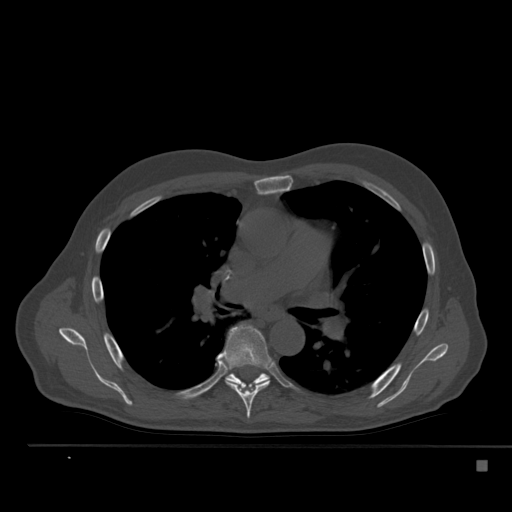
CT including the spine, one axial slice. Slice 340 of 517 in the series (ordered by position). Reconstruction kernel Br40s. Bone window (W 1800 / L 400 HU). 1.5 mm slice thickness. 512 × 512 image matrix, field of view 408 × 408 mm. Male patient, age 70 years. From the clinical record (not read from this slice): primary cancer: renal.
Annotated regions visible in this slice (semi-automatic segmentation, software-assisted and operator-edited):
- T6 vertebra: box from (x=219, y=324) to (x=273, y=419) px
- T7 vertebra: (x=225, y=373)–(x=270, y=388)